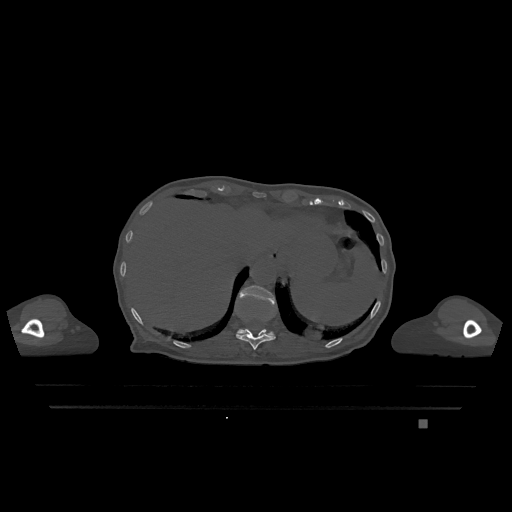
CT including the spine, one axial slice; slice 572 of 1317 in the series (ordered by position); bone window (W 1800 / L 400 HU); 0.5 mm slice thickness; 512 × 512 image matrix, field of view 500 × 500 mm. Female patient, age 74 years. Case-level facts recorded for this patient, not image findings: primary cancer: lung.
Outlined on this slice (semi-automatic segmentation, software-assisted and operator-edited):
- T11 vertebra: bounding box [x1, y1, x2, y2] px = [236, 316, 276, 350]
- T12 vertebra: [238, 285, 276, 337]